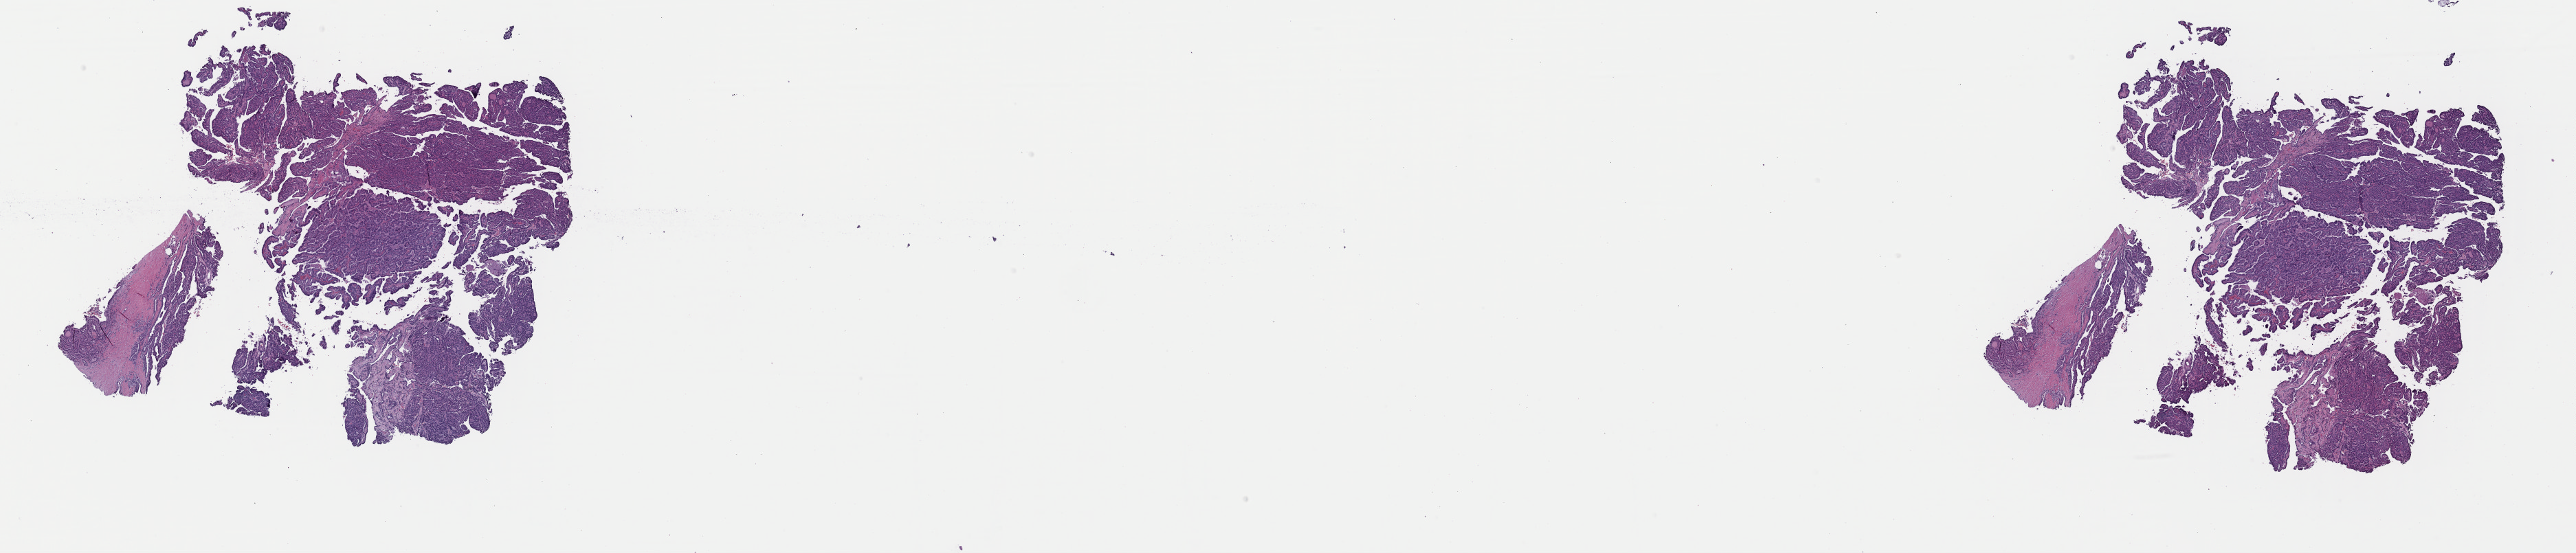
Whole-slide histology image, H&E, low-resolution overview of the scanned area, about 29.6 x 6.4 mm, formalin-fixed paraffin-embedded (FFPE) diagnostic section, sample: primary tumour, thyroid. Patient: female, age at initial diagnosis 29 years.
Diagnosis: Papillary adenocarcinoma, NOS (thyroid gland).